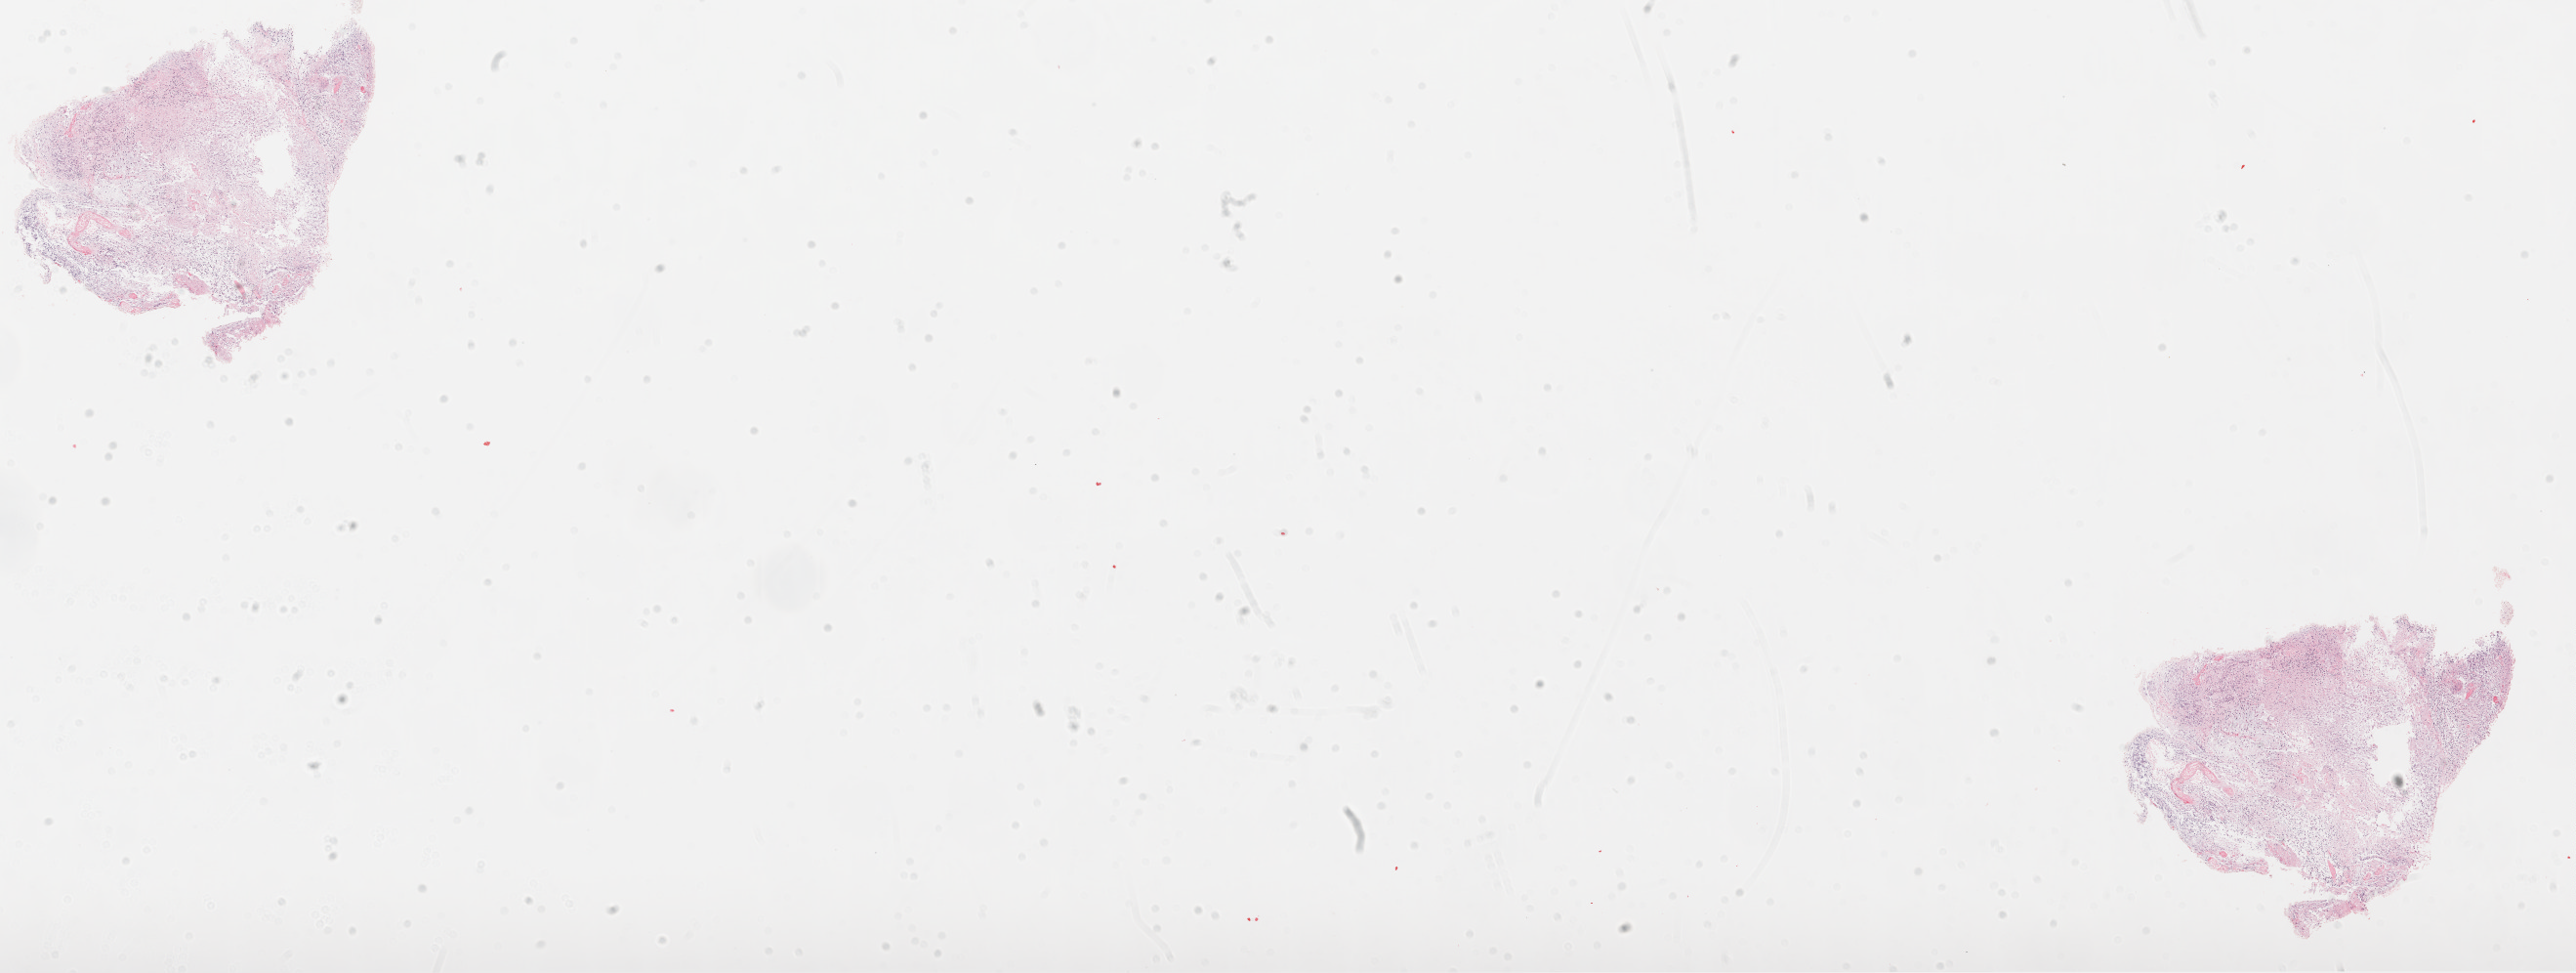
H&E-stained whole-slide image — a low-resolution overview of the entire scanned area, about 21.3 x 8.0 mm (slide scanned at 20x); formalin-fixed paraffin-embedded (FFPE) diagnostic section; brain, primary tumour sample. Male, age 54 years at initial diagnosis.
* diagnosis: Glioblastoma